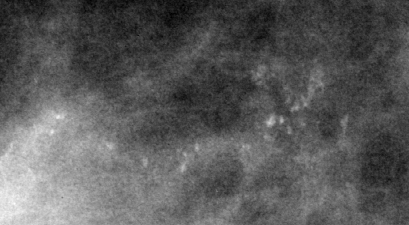
Crop from a digitized film mammogram around one marked abnormality; right breast; MLO view; BI-RADS breast density category 3 (scale 1–4).
Marked abnormality: calcifications, morphology pleomorphic, distribution clustered / linear; BI-RADS assessment category 4; pathology (as recorded): benign.